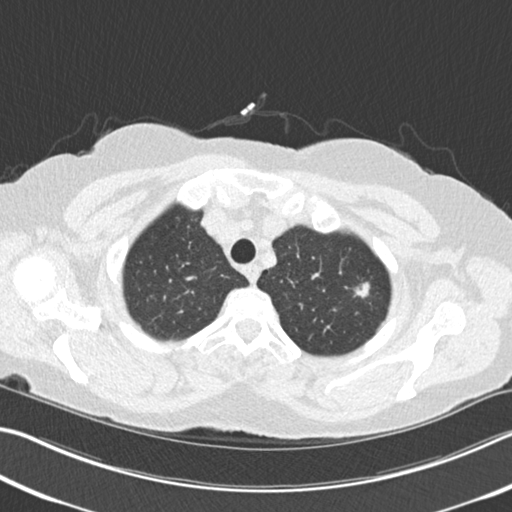
Chest CT (low-dose screening protocol), one axial image; second screening round (one year after baseline); lung window (W 1500 / L -600 HU); standard (soft-tissue) reconstruction kernel (B30f); slice 31 of 225 in the series; 512 × 512 image matrix. Female participant, aged 64 years at enrolment.
Lesion marked by an expert reader, bounding box (x1, y1, x2, y2) in pixels: (344, 273, 377, 305). Screening reader's record for this exam (one nodule recorded; not confirmed to be the boxed lesion): non-calcified nodule or mass ≥4 mm, left upper lobe, 13 × 10 mm, spiculated (stellate) margins, soft tissue attenuation, pre-existing on the prior screen: yes; interval growth: yes. Participant outcome: lung cancer diagnosed 106 days after this screen — signet ring cell carcinoma, right upper lobe, poorly differentiated (G3), stage IA (AJCC 6th edition), 15 mm at pathology.